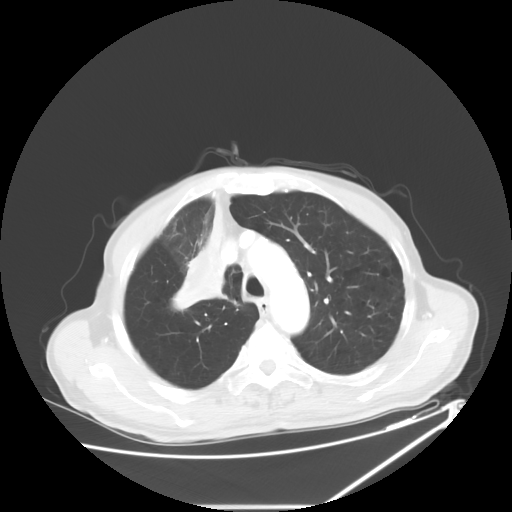
Chest CT, one axial slice; slice 46 of 60 in the series (ordered by position); 120 kVp; lung window (W 1500 / L -600 HU); 5 mm slice thickness; 512 × 512 image matrix. Patient: male, 73 years. Case-level facts recorded for this patient, not image findings: clinical TNM (as recorded): T2a N1 M0.
Structures marked on this image (rectangle marked by the reading radiologist):
- lung tumour (recorded histology: squamous cell carcinoma): bounding box (x1, y1, x2, y2) in pixels: (169, 186, 232, 312)